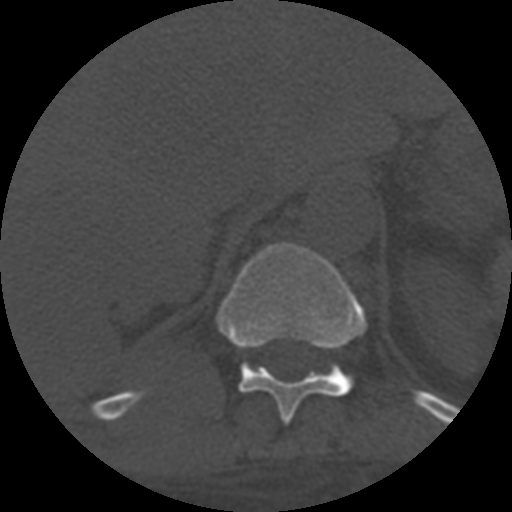
CT including the spine, one axial slice. 120 kVp. One of 3 acquisitions stored at this slice position. Bone window (W 1800 / L 400 HU). 1.25 mm slice thickness. 512 × 512 image matrix, field of view 160 × 160 mm. Patient age 55 years. From the clinical record (not read from this slice): primary cancer: colon.
Outlined on this slice (semi-automatic segmentation, software-assisted and operator-edited):
- T11 vertebra: bounding box [x1, y1, x2, y2] px = [216, 243, 368, 423]